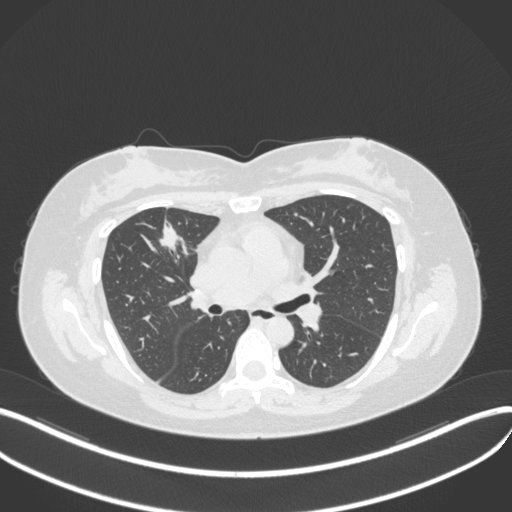
Chest CT, one axial slice. Slice 184 of 272 in the series (ordered by position). Reconstruction kernel B31f. Lung window (W 1500 / L -600 HU). 1 mm slice thickness. 512 × 512 image matrix. Female patient, age 42 years. From the clinical record (not read from this slice): clinical TNM (as recorded): T1b N0 M0.
Structures marked on this image (rectangle marked by the reading radiologist):
- lung tumour (recorded histology: adenocarcinoma): bounding box (x1, y1, x2, y2) in pixels: (155, 214, 191, 260)